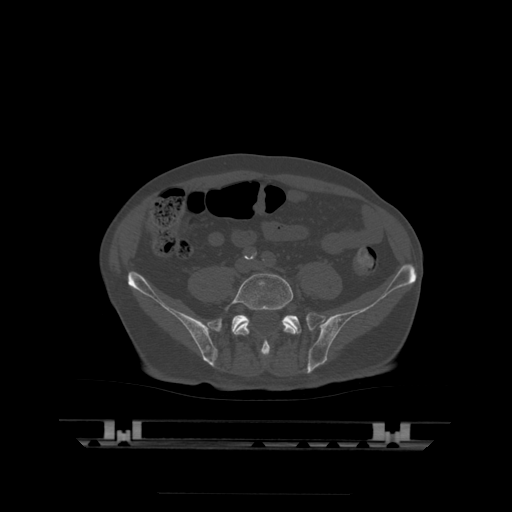
CT including the spine, one axial slice. Slice 67 of 522 in the series (ordered by position). Bone window (W 1800 / L 400 HU). 1.25 mm slice thickness. 512 × 512 image matrix. Patient age 68 years. Case-level facts recorded for this patient, not image findings: primary cancer: urothelial.
Annotated regions visible in this slice (semi-automatic segmentation, software-assisted and operator-edited):
- L5 vertebra: box from (x=226, y=273) to (x=296, y=356) px